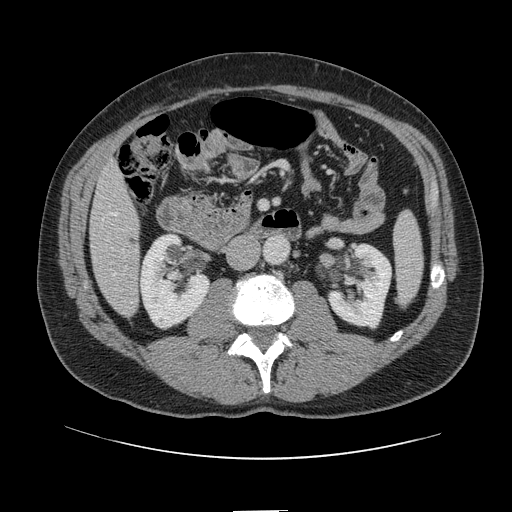
Contrast-enhanced abdominal CT, one axial slice. Position 29 of 161 along the scan axis. 120 kVp. Intravenous contrast given. Soft-tissue window (W 400 / L 40 HU). 2.5 mm slice thickness. 512 × 512 image matrix, field of view 412 × 412 mm. Male patient, age 66 years. Case-level facts recorded for this patient, not image findings: diagnosis: colorectal cancer liver metastases, imaged before liver resection; multiple liver metastases: no; largest metastasis: 3.5 cm; disease in both lobes: no.
Annotated regions visible in this slice (manually delineated by an expert):
- hepatic veins: bounding box <114,213,117,275> (left, top, right, bottom; pixels)
- liver: <92,165,140,316>
- planned liver remnant (the part of the liver to remain after resection): <92,165,140,259>